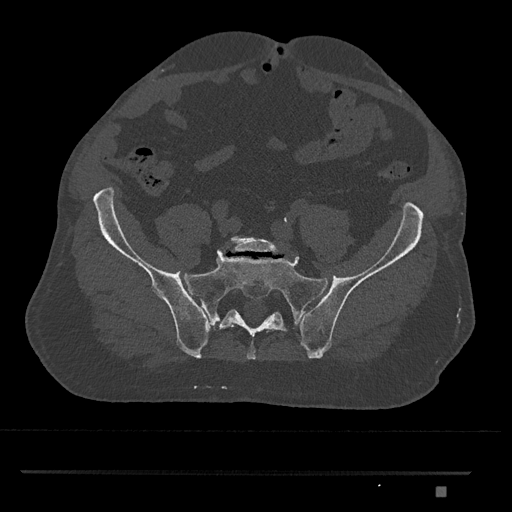
CT including the spine, one axial slice. Position 498 of 1134 along the scan axis. Reconstruction kernel Br40s/3. 120 kVp. Bone window (W 1800 / L 400 HU). 0.5 mm slice thickness. 512 × 512 image matrix, field of view 429 × 429 mm. Male patient, age 65 years. Case-level facts recorded for this patient, not image findings: primary cancer: prostate.
Outlined on this slice (semi-automatically segmented with operator editing):
- L5 vertebra: bounding box <229,236,287,253> (left, top, right, bottom; pixels)